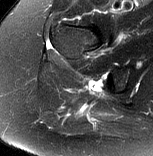
MRI of an extremity soft-tissue mass, one axial slice. Position 56 of 77 along the scan axis. T2-weighted fat-saturated. MR volume resampled by the dataset authors to the PET/CT grid (not the native acquisition matrix). 3.27 mm slice thickness. 153 × 156 image matrix. Female patient. Case-level facts recorded for this patient, not image findings: histological type: synovial sarcoma; grade: intermediate; site of the primary tumour: right buttock.
Outlined on this slice (expert contour drawn on MRI and transferred to this co-registered scan by the dataset authors):
- gross tumour volume including surrounding oedema: bounding box (x1, y1, x2, y2) in pixels: (76, 104, 90, 114)